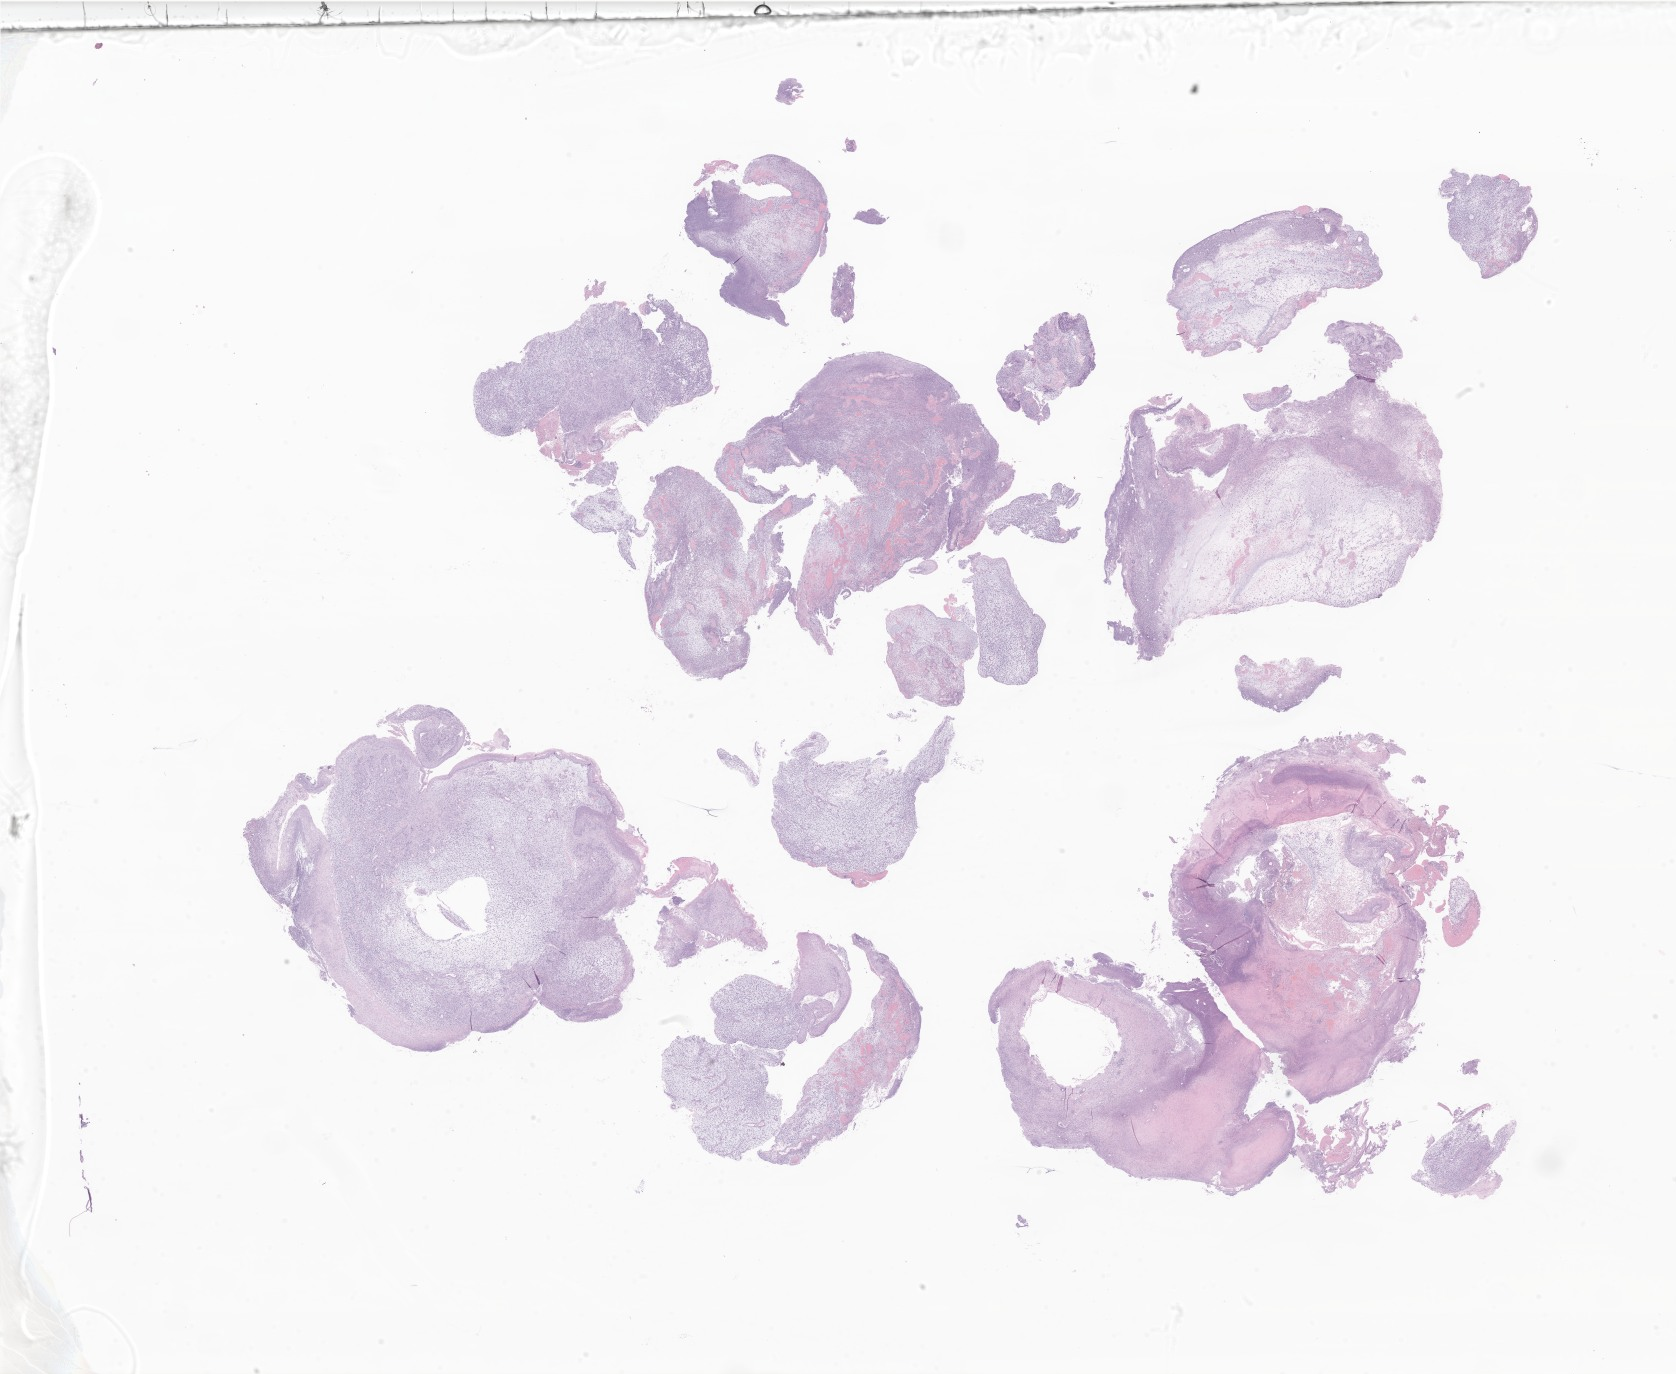
Whole-slide image, haematoxylin and eosin stain of tumor tissue from the external ear, whole scanned area (about 28.3 x 23.2 mm) shown as a low-resolution overview. FFPE section. Male patient, age 54 months.
Diagnosis: Embryonal rhabdomyosarcoma, NOS.